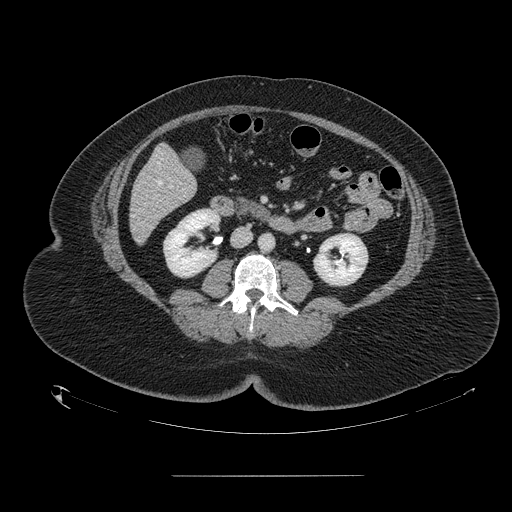
Contrast-enhanced abdominal CT, one axial slice; position 46 of 164 along the scan axis; 120 kVp; intravenous contrast given; soft-tissue window (W 400 / L 40 HU); 2.5 mm slice thickness; 512 × 512 image matrix, field of view 495 × 495 mm. Female patient, age 52 years. Case-level facts recorded for this patient, not image findings: diagnosis: colorectal cancer liver metastases, imaged before liver resection; multiple liver metastases: yes; largest metastasis: 3.5 cm; disease in both lobes: no.
Structures marked on this image (outlined manually by an expert reader):
- hepatic veins: box from (x=157, y=162) to (x=161, y=184) px
- liver: (x=130, y=145)–(x=196, y=243)